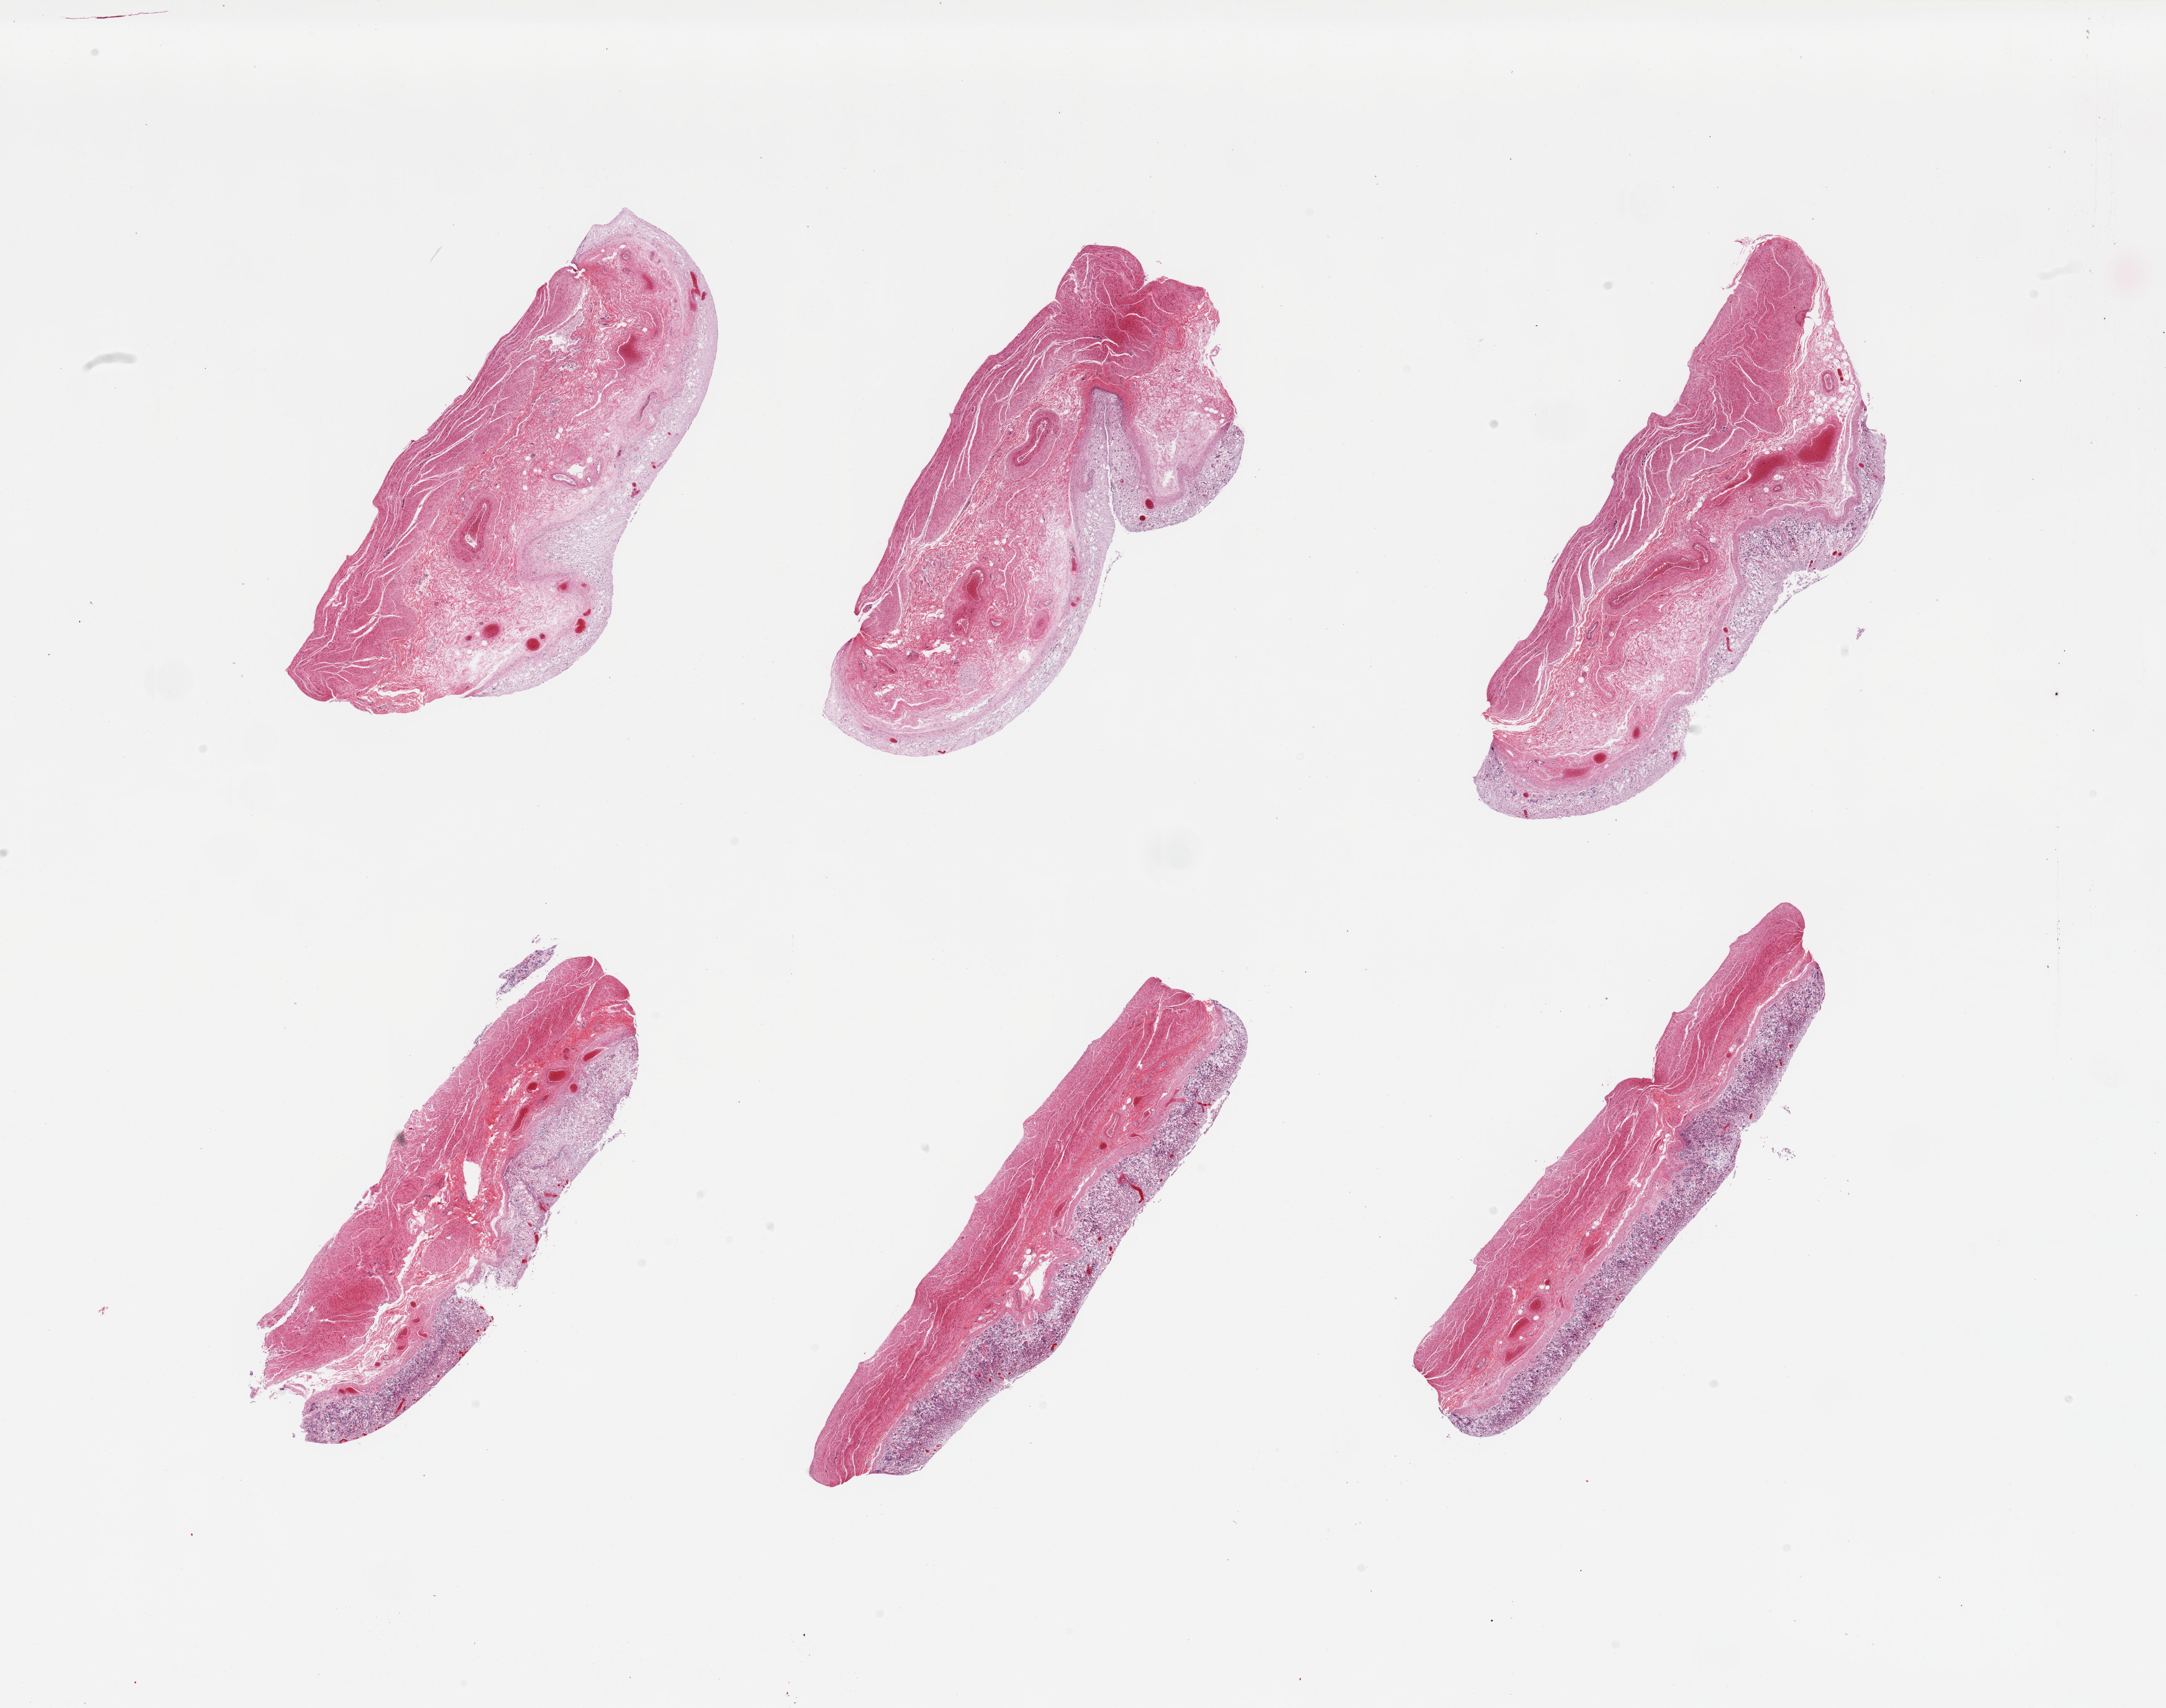
H&E whole-slide image — low-resolution overview of the scanned area, about 27.6 x 21.7 mm, PAXgene-fixed paraffin-embedded (PFPE) section, sampled site (target tissue): stomach, tissue donor sample. Donor: female.
Reviewer comment on this tissue sample: 6 pieces; mucosa completely autolyzed; muscularis is OK (=1).